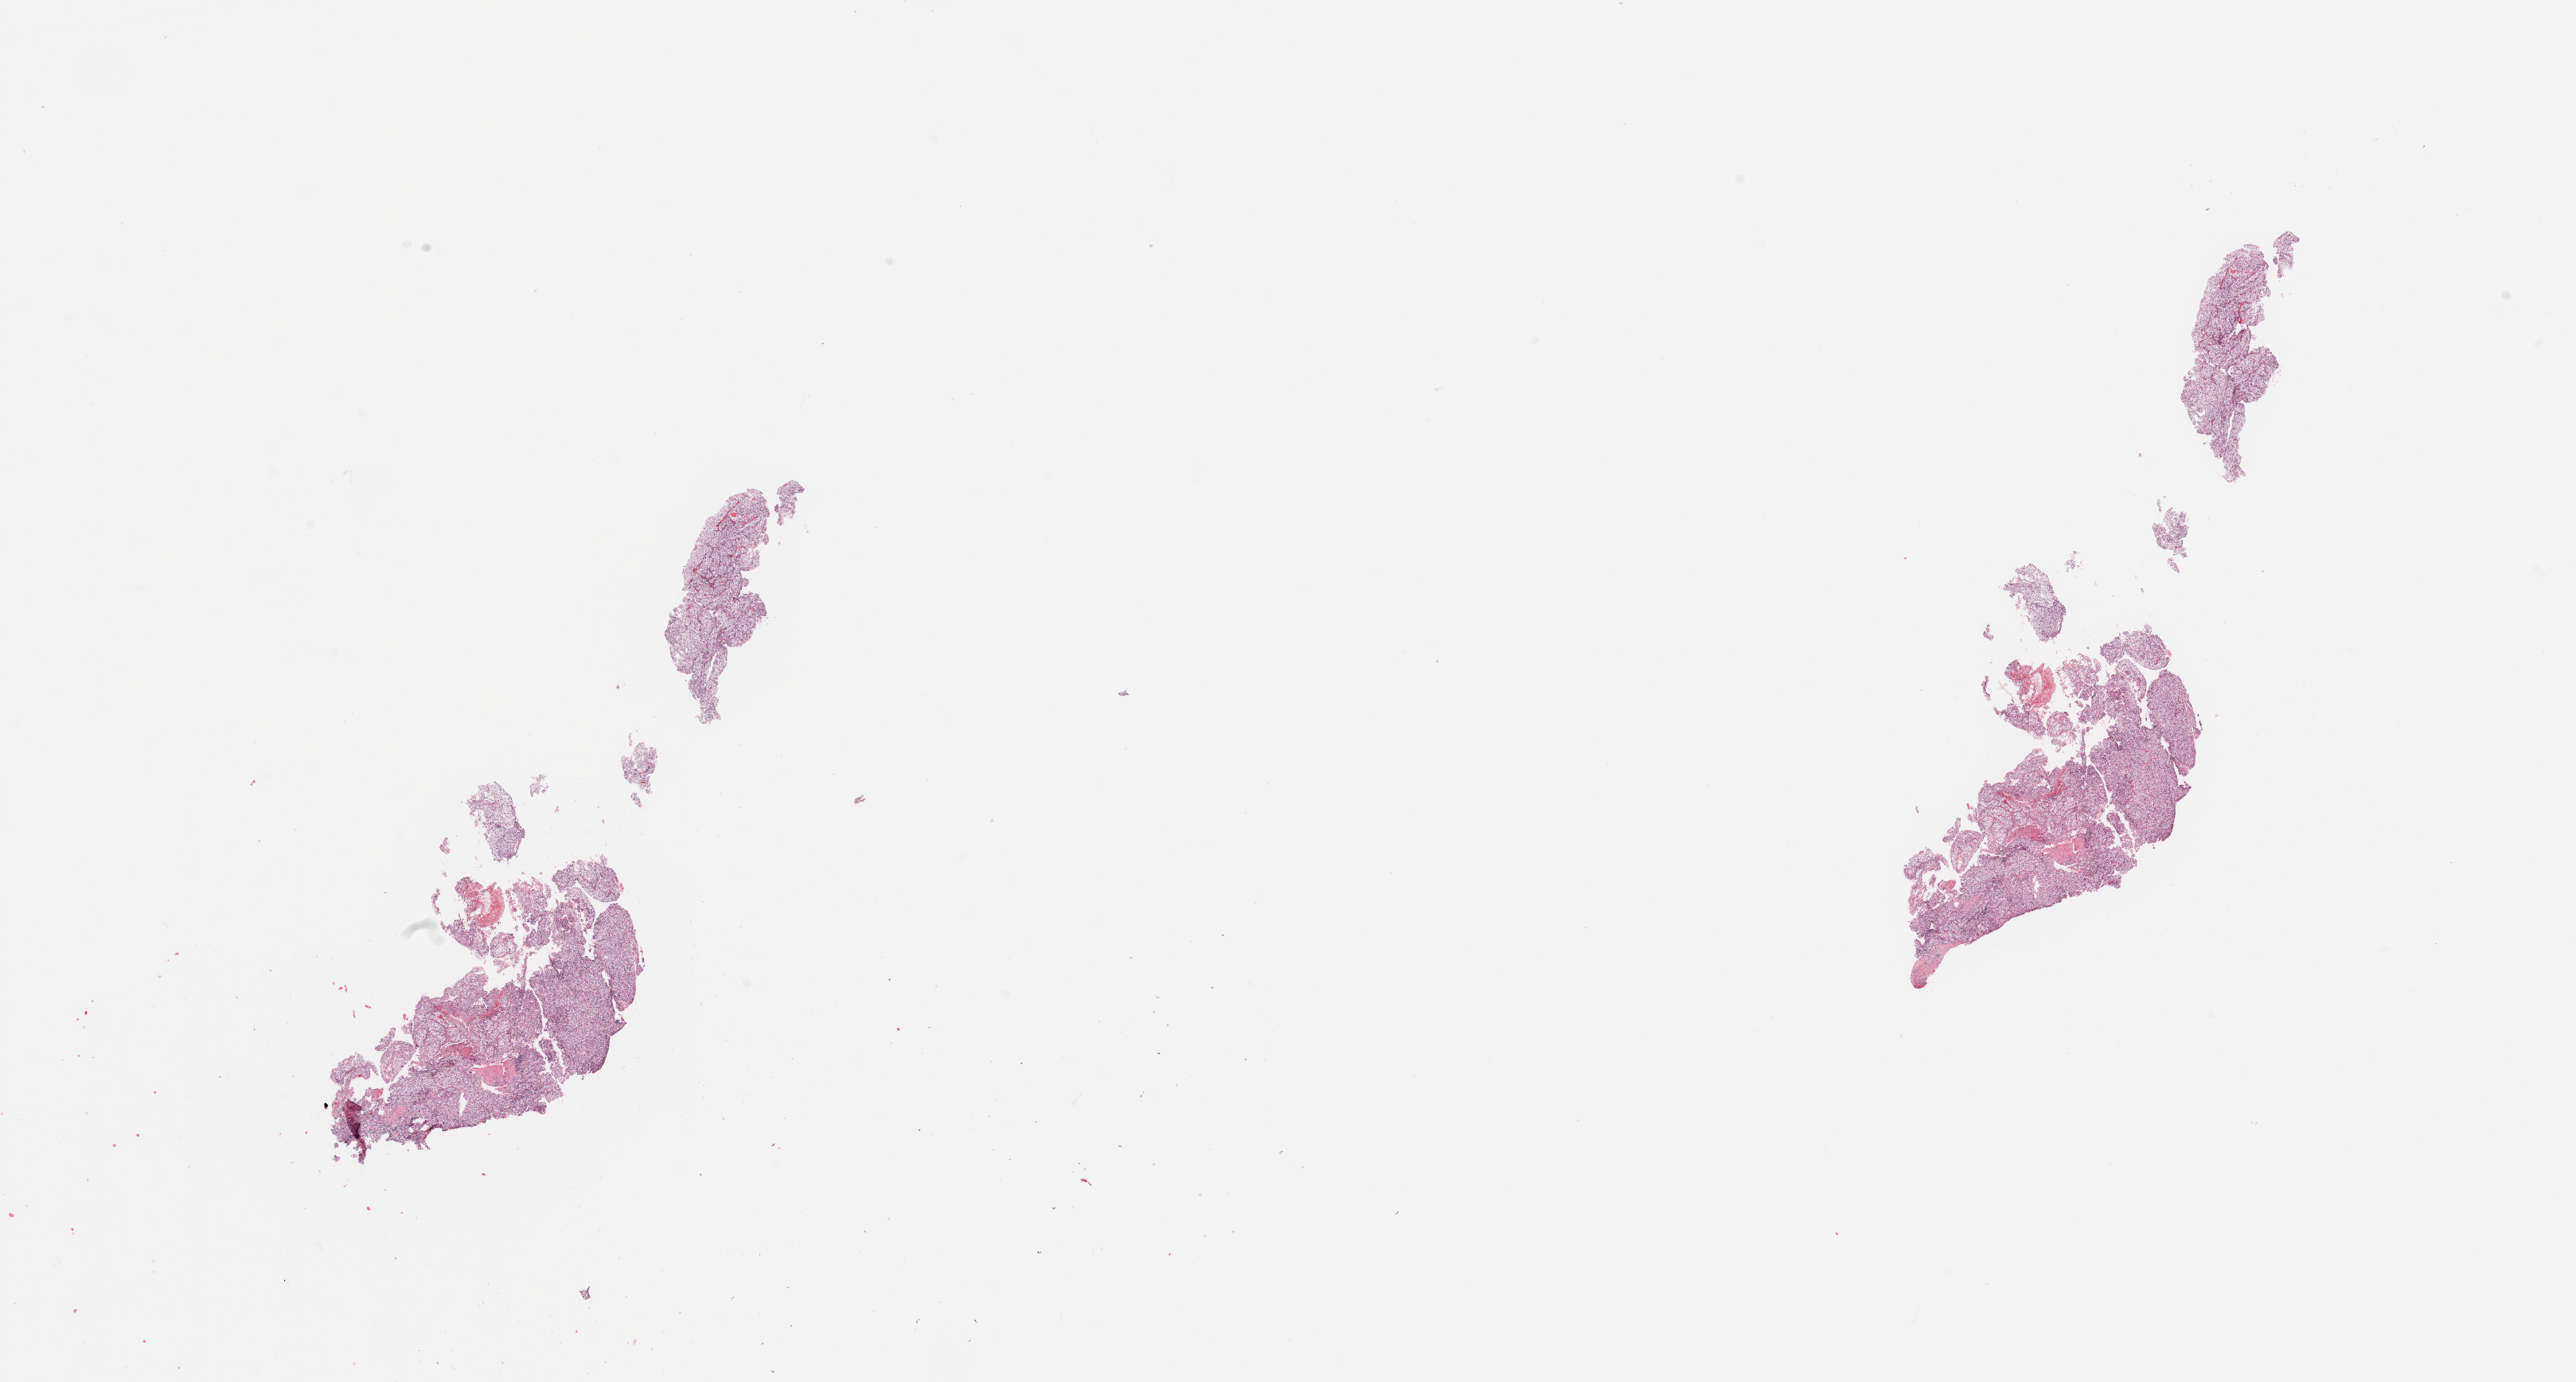
H&E whole-slide image — a low-resolution overview of the entire scanned area, about 25.6 x 13.7 mm, tumour tissue sample, sampled site: kidney. 44-year-old male patient. Histologic grade: G2 (moderately differentiated). Pathologist review of this section (percent, as recorded): tumour nuclei 95%, necrosis 5%.
Histologic diagnosis: Renal cell carcinoma, NOS. AJCC pathologic stage: I. Primary tumour site (as recorded): lower pole.